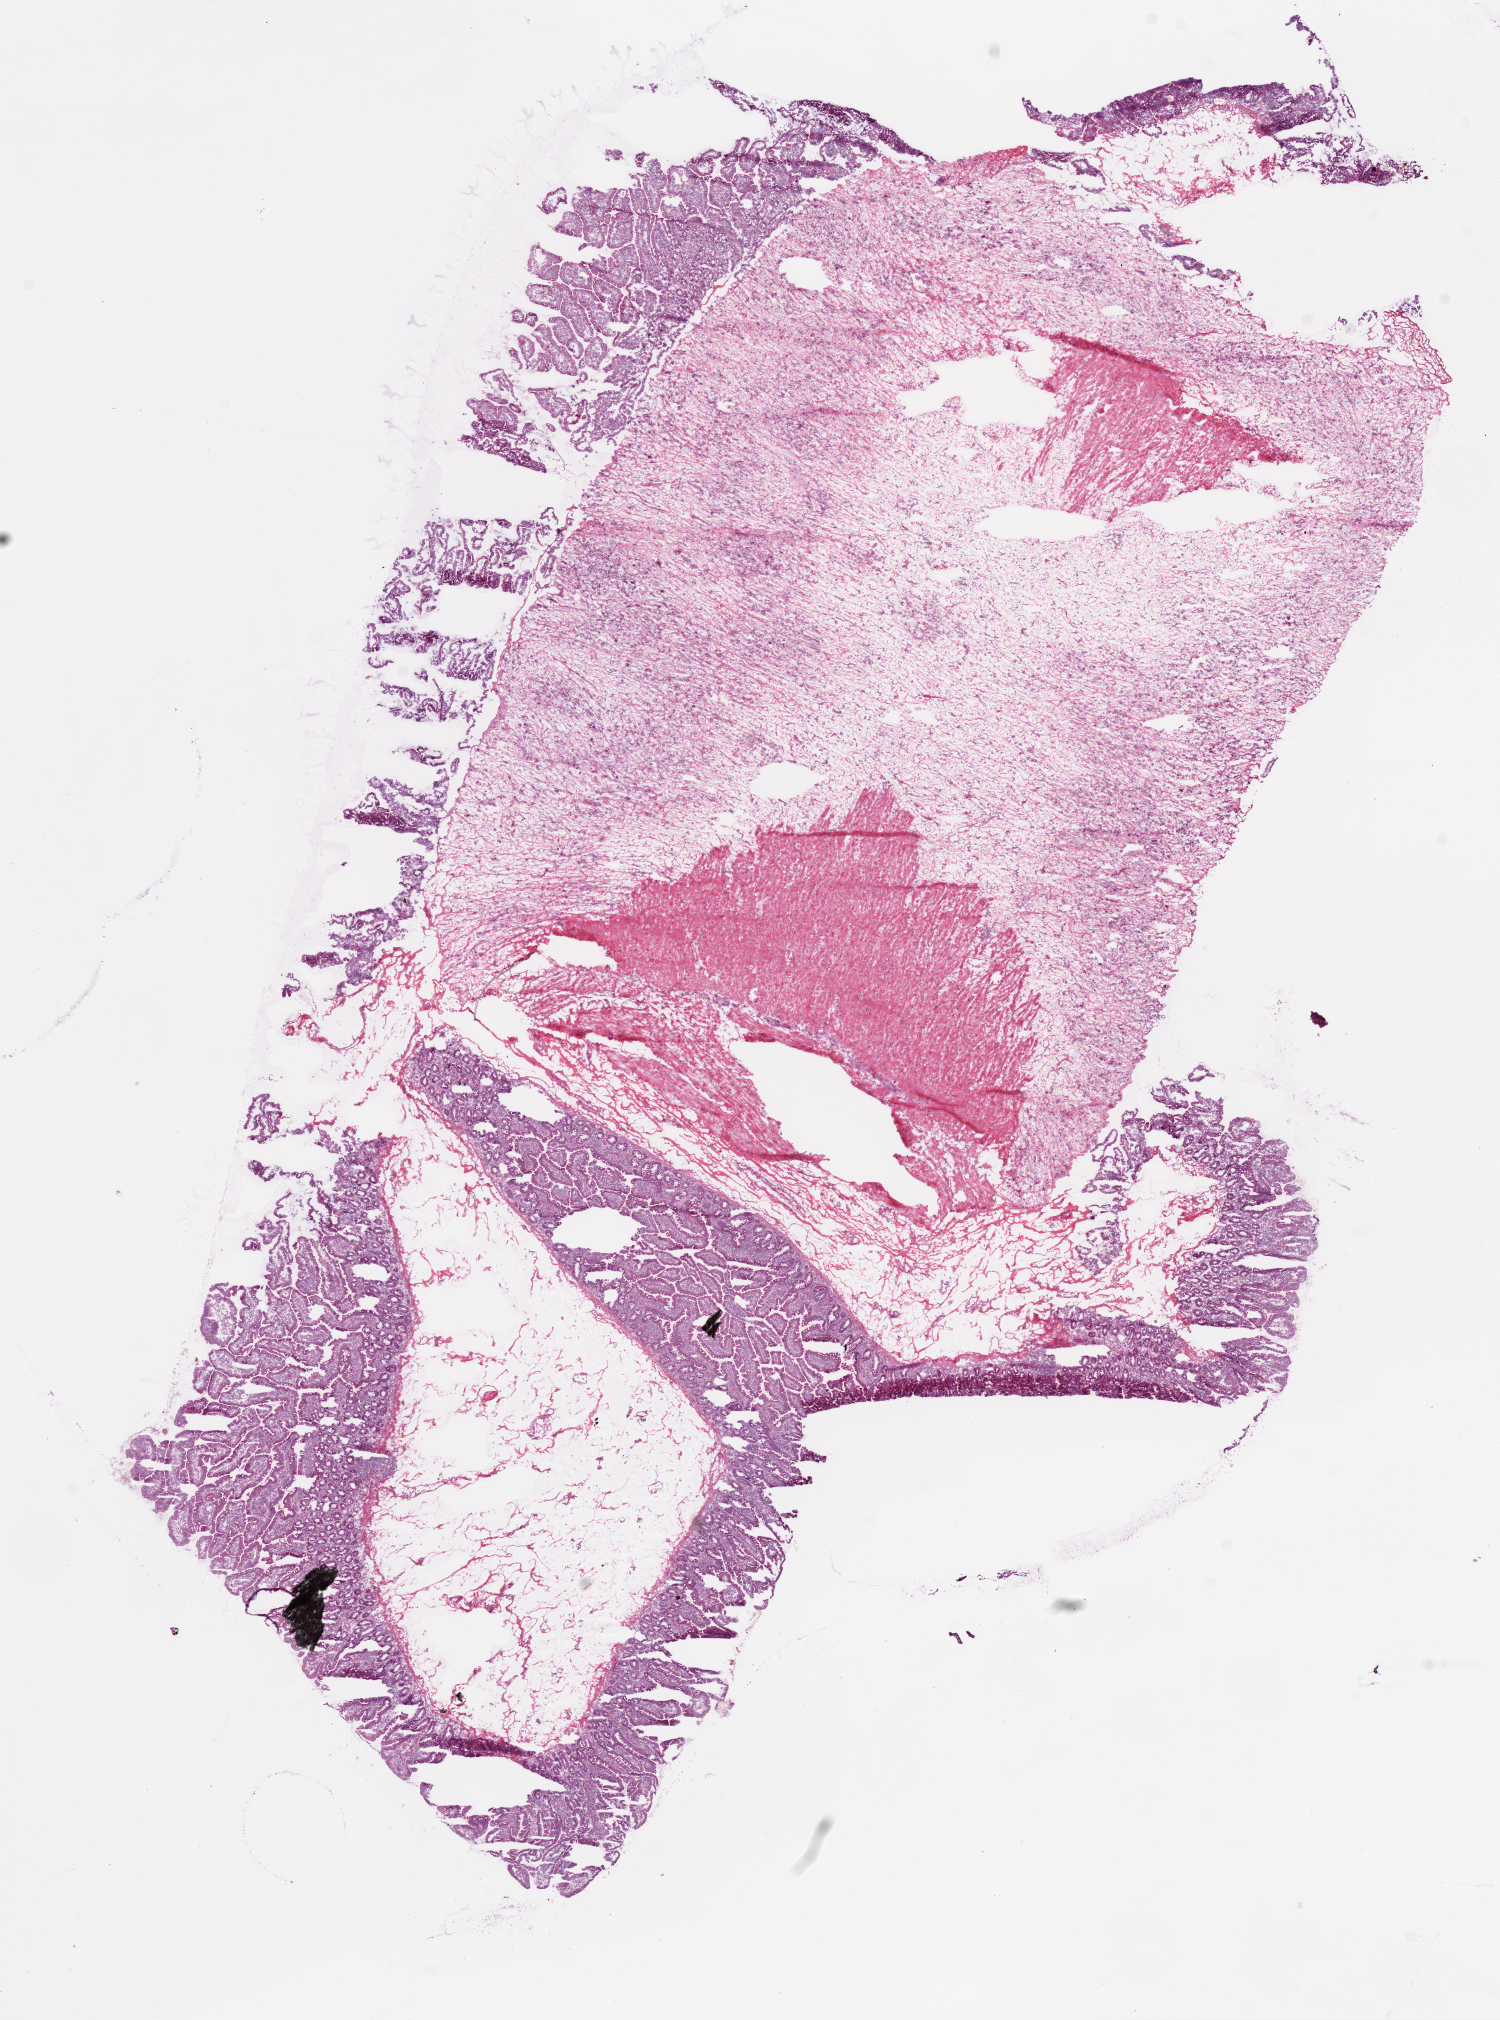
Whole-slide histology image, Hematoxylin and eosin (H&E) stained — shown as a low-resolution overview of the whole scanned area (about 12.0 x 16.2 mm, acquisition: 20x scan); frozen section from the bottom of the tissue portion; solid tissue normal (non-tumour tissue) sample from the ovary. Female, age 40 years at initial diagnosis.
This section: solid tissue normal sample (biorepository sample class). Patient diagnosis: Serous cystadenocarcinoma, NOS.